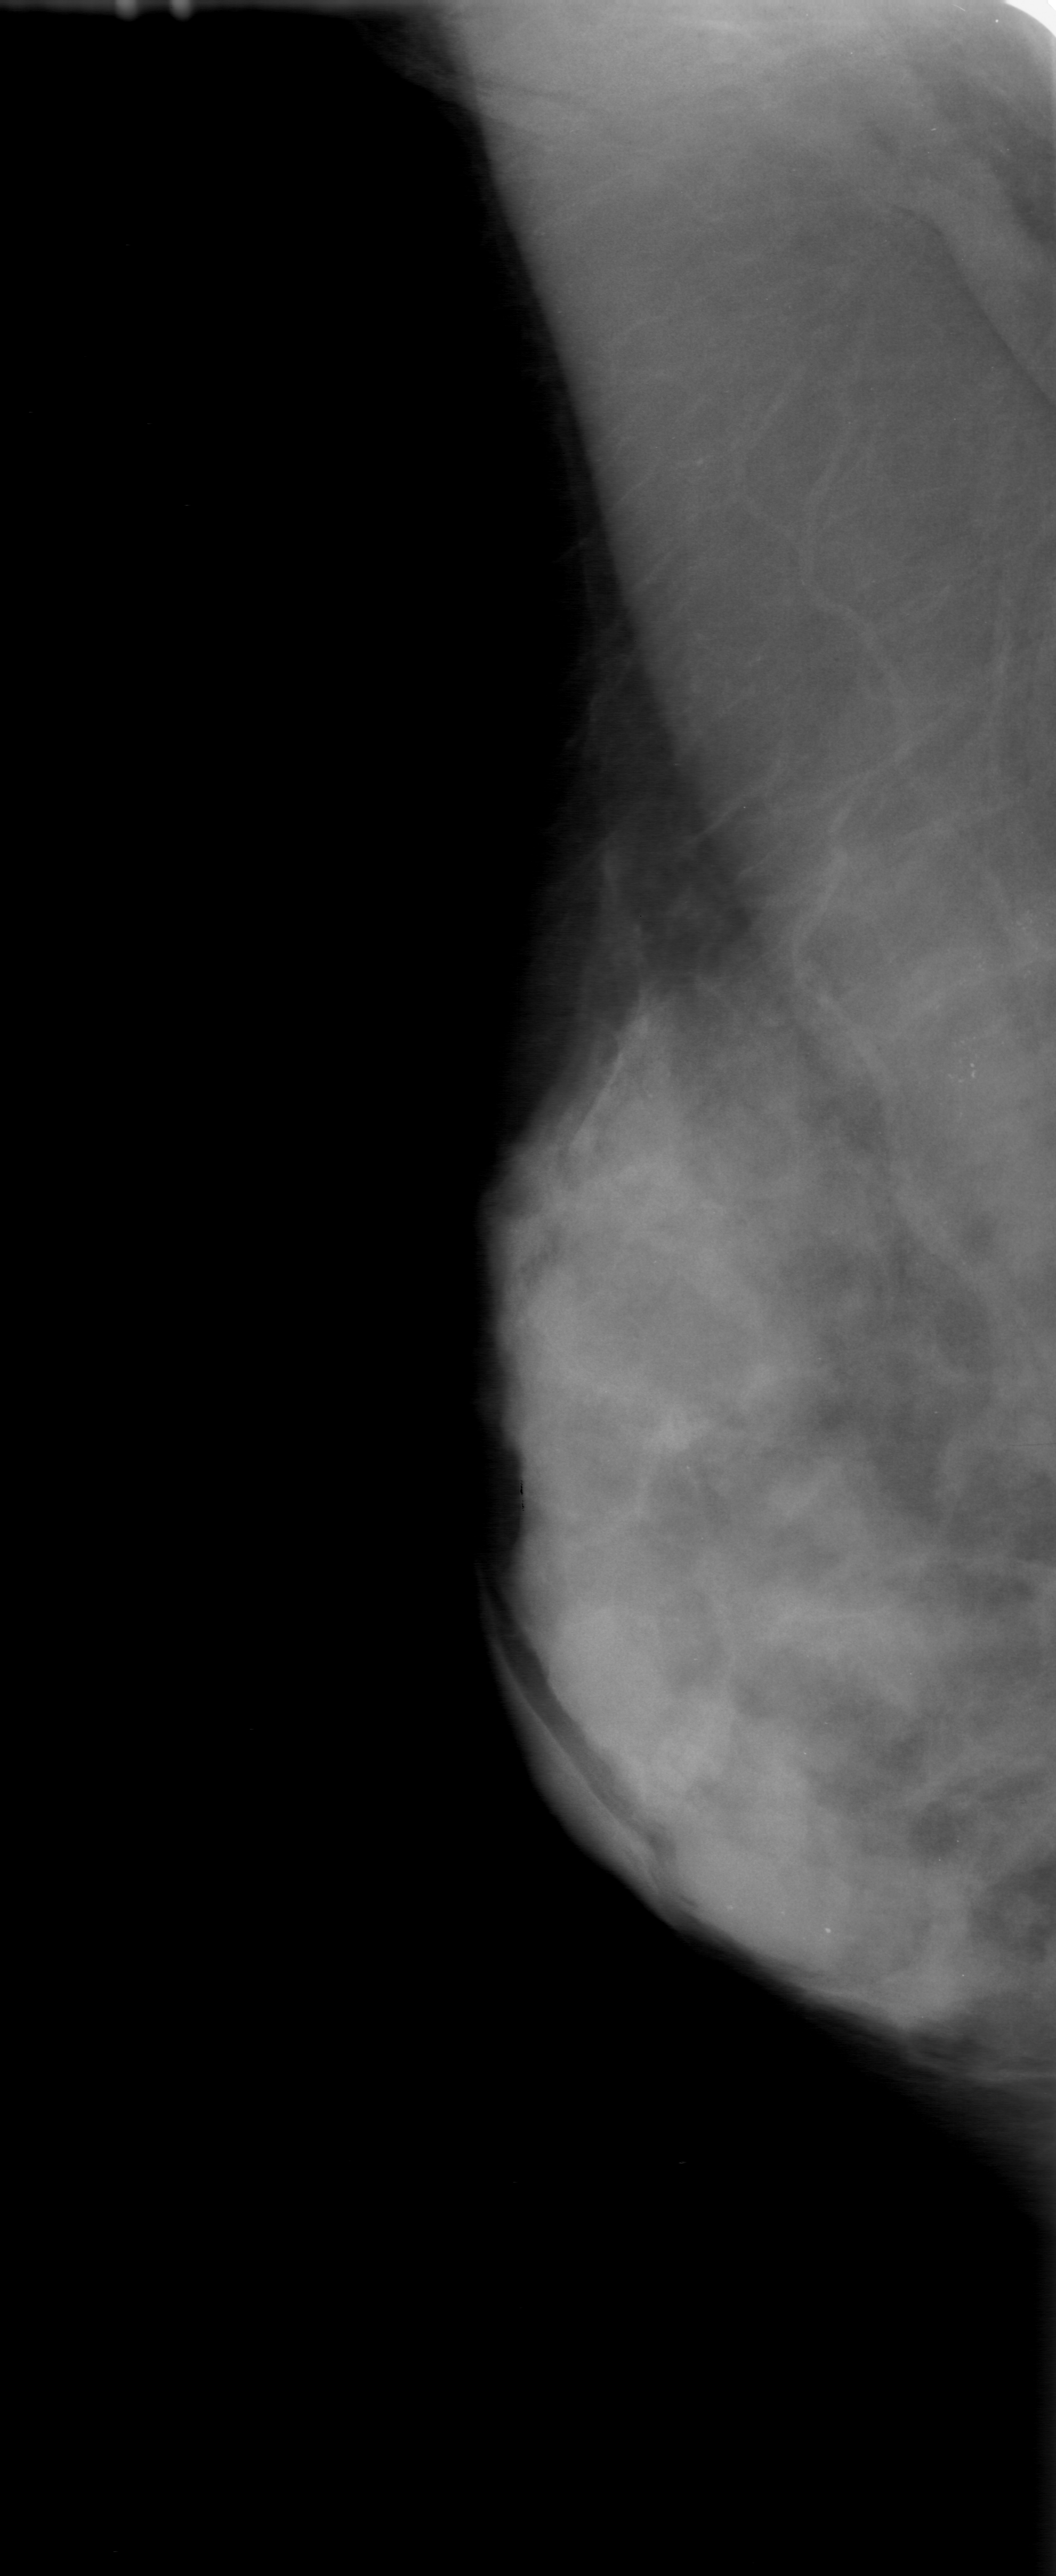
Digitized screen-film mammogram; right breast; mediolateral oblique (MLO) view; breast composition: extremely dense (BI-RADS density category 4 of 4); 1056 × 2576 image matrix.
Marked abnormalities (boxes around the expert regions of interest):
- calcifications, morphology pleomorphic, distribution clustered; BI-RADS assessment category 0 (incomplete: needs additional imaging); subtlety rating 4 on a 1 (subtle) to 5 (obvious) scale; pathology result (as recorded, not read from the image): malignant: box from (x=825, y=852) to (x=1056, y=1218) px